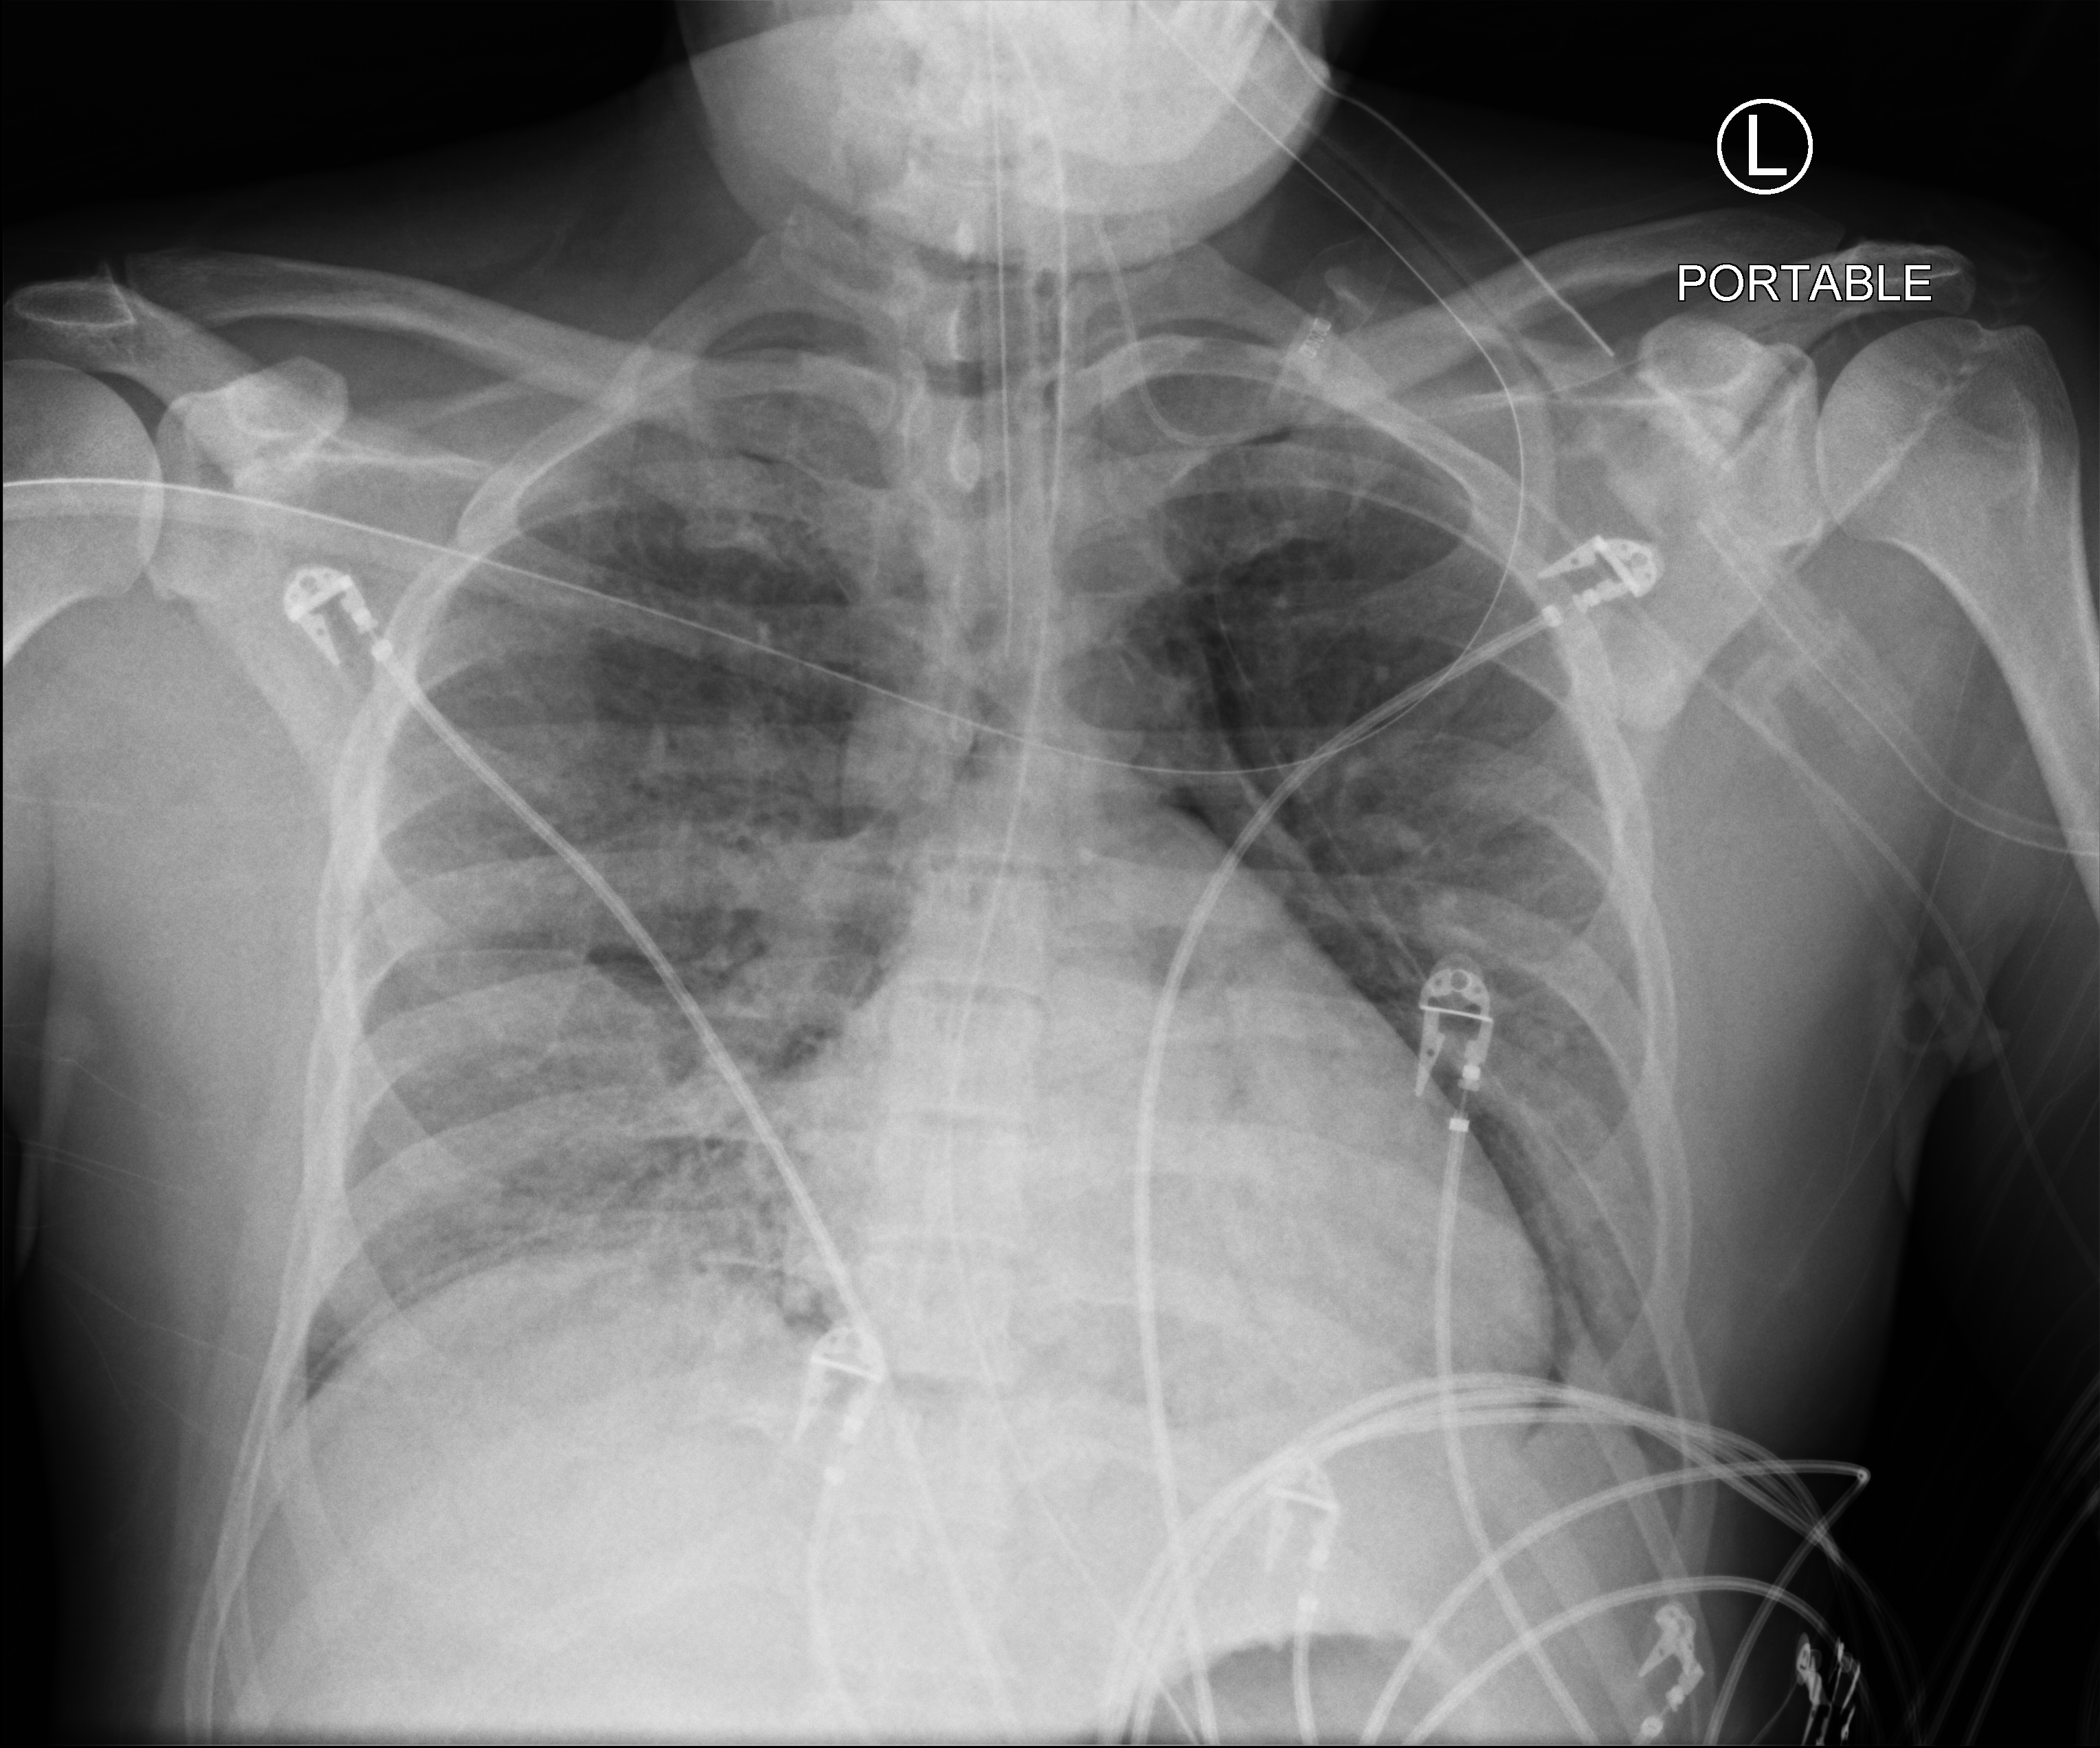
Chest X-ray (portable); anteroposterior (AP) projection. Male patient hospitalised with COVID-19, age 18–59 years.
From the hospital-stay record, not from the radiograph (when in the stay this image was taken is not recorded):
- mechanically ventilated during this hospital stay: yes